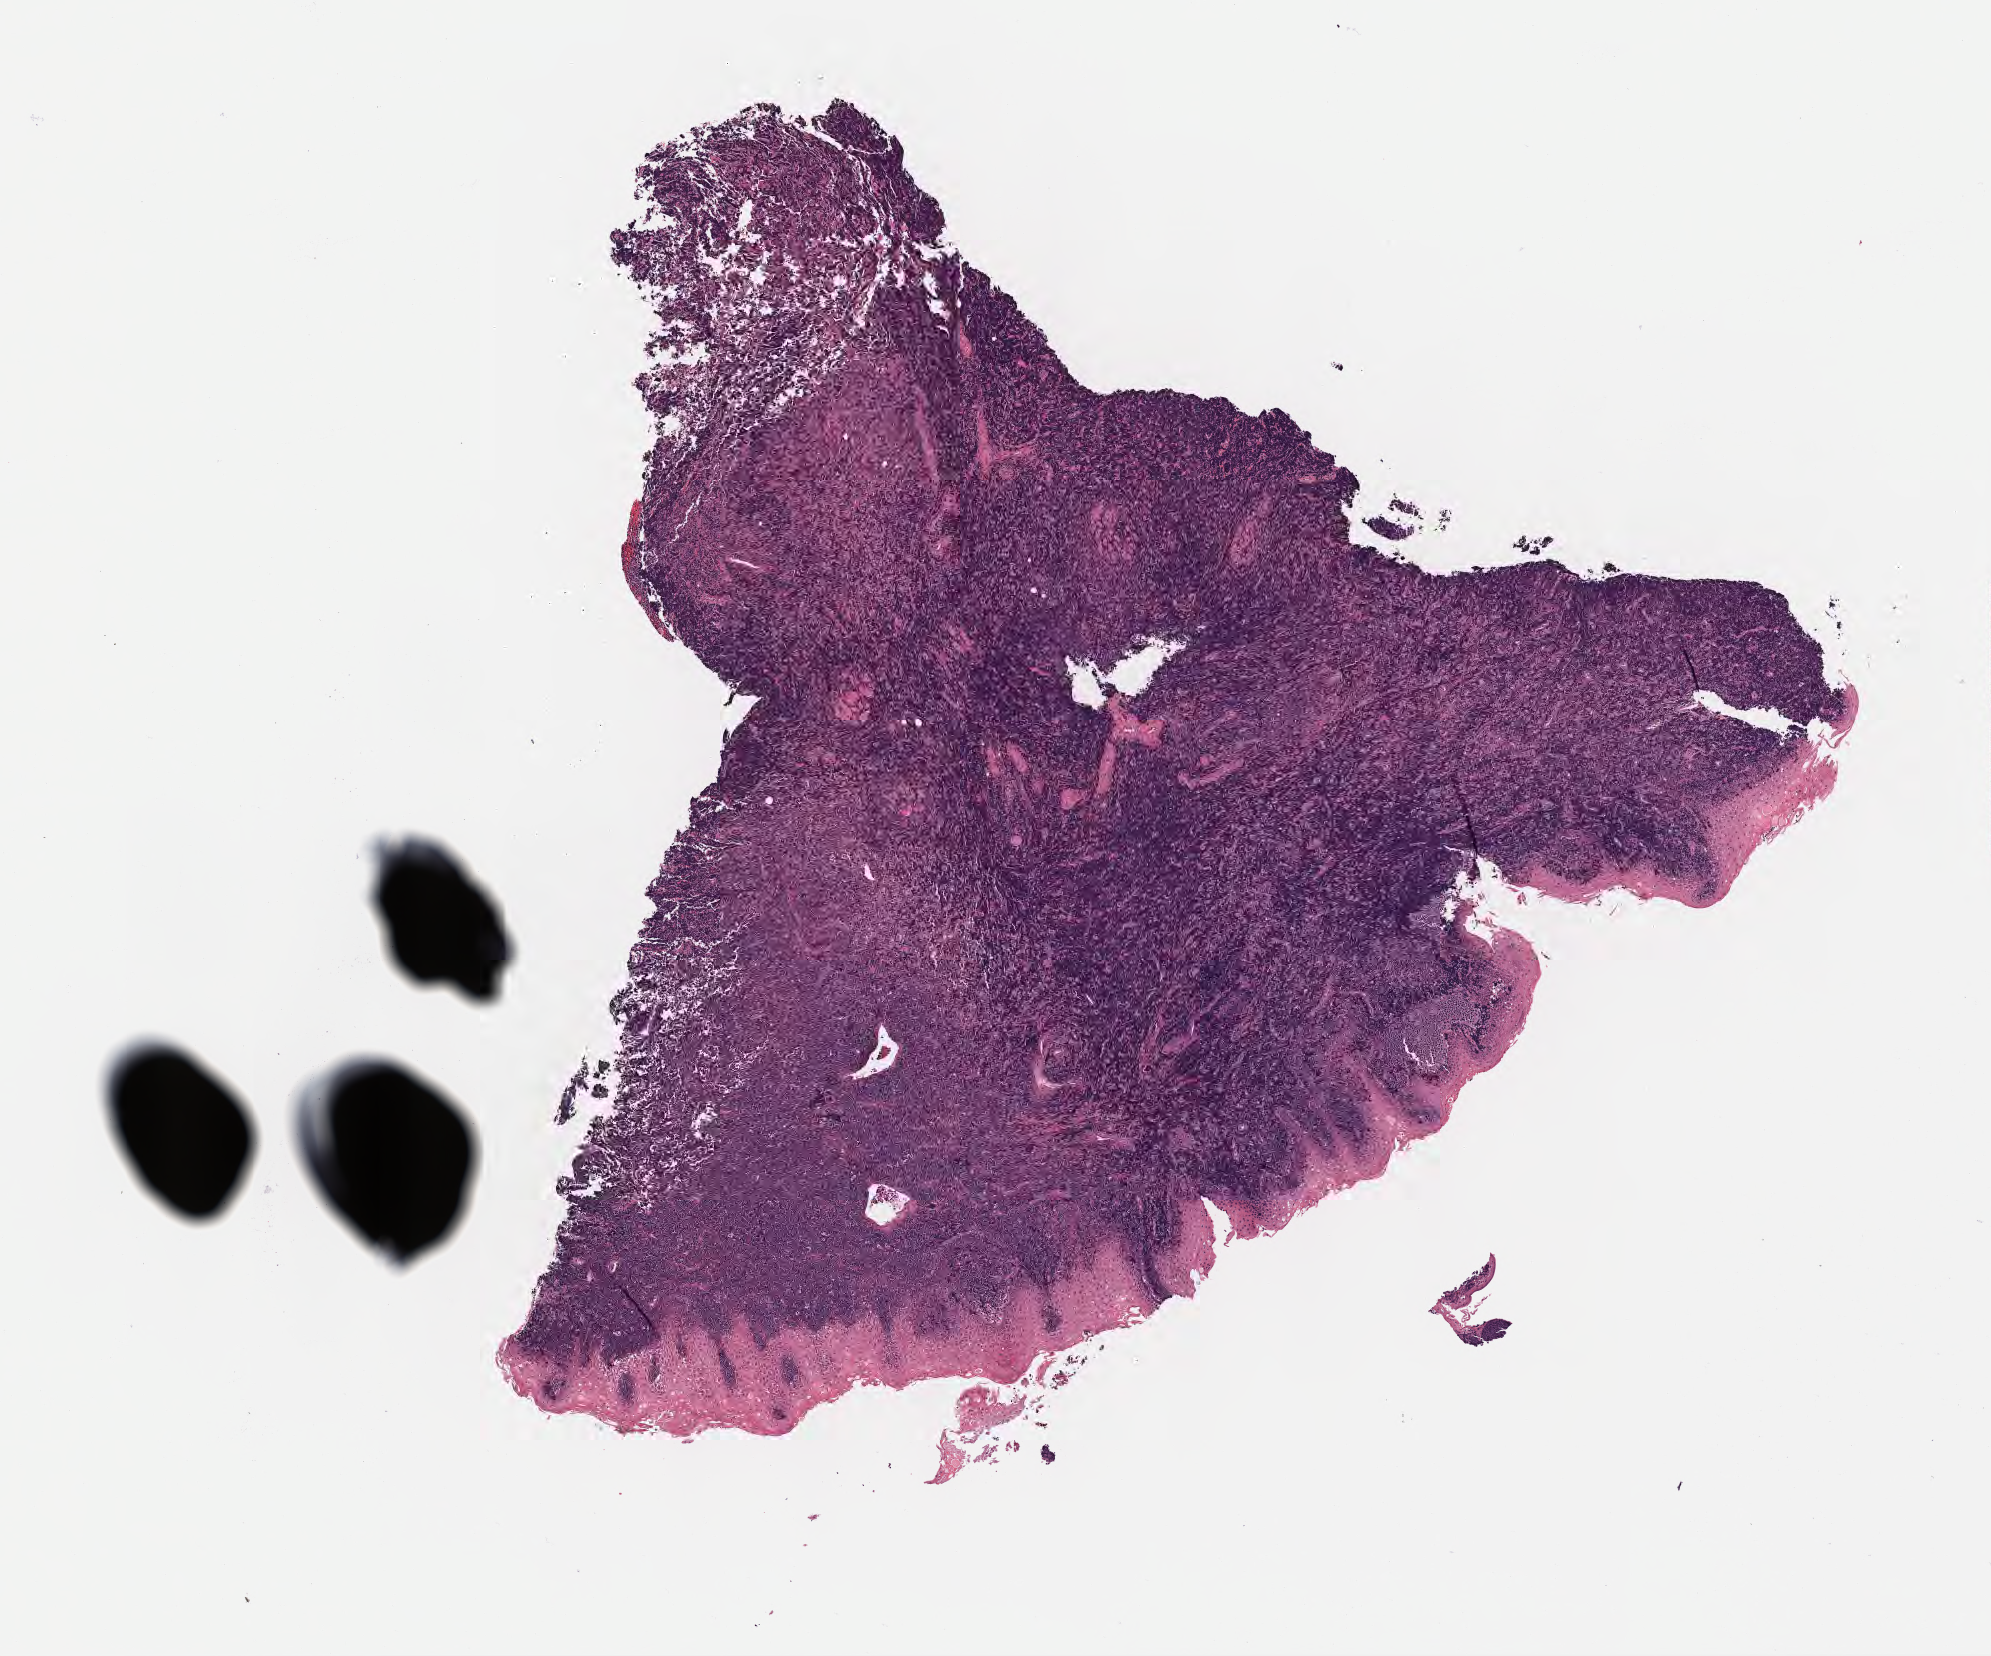
Whole-slide image, H&E stain, a low-resolution overview of the entire scanned area, about 8.1 x 6.7 mm; specimen: tumor tissue; anatomic site: cranium. Male patient; age at initial diagnosis 8 years.
Diagnosis: Diffuse large B-cell lymphoma, NOS.